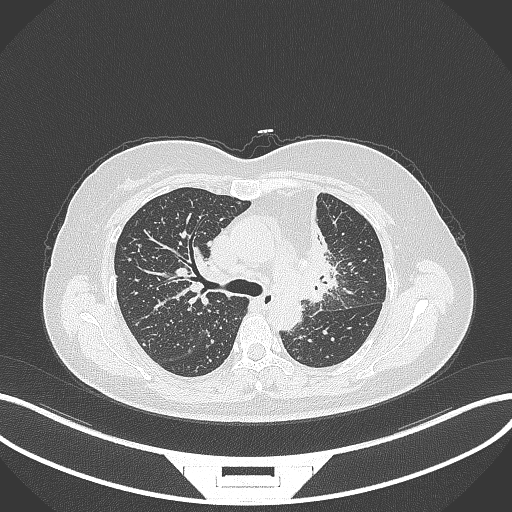
Chest CT, one axial slice. Slice 220 of 348 in the series (ordered by position). Lung window (W 1500 / L -600 HU). 512 × 512 image matrix, field of view 400 × 400 mm. Patient: female, 49 years. Case-level facts recorded for this patient, not image findings: clinical TNM (as recorded): T1c N0 M1.
Outlined on this slice (rectangle marked by the reading radiologist):
- lung tumour (recorded histology: adenocarcinoma): bounding box (x1, y1, x2, y2) in pixels: (290, 191, 341, 304)